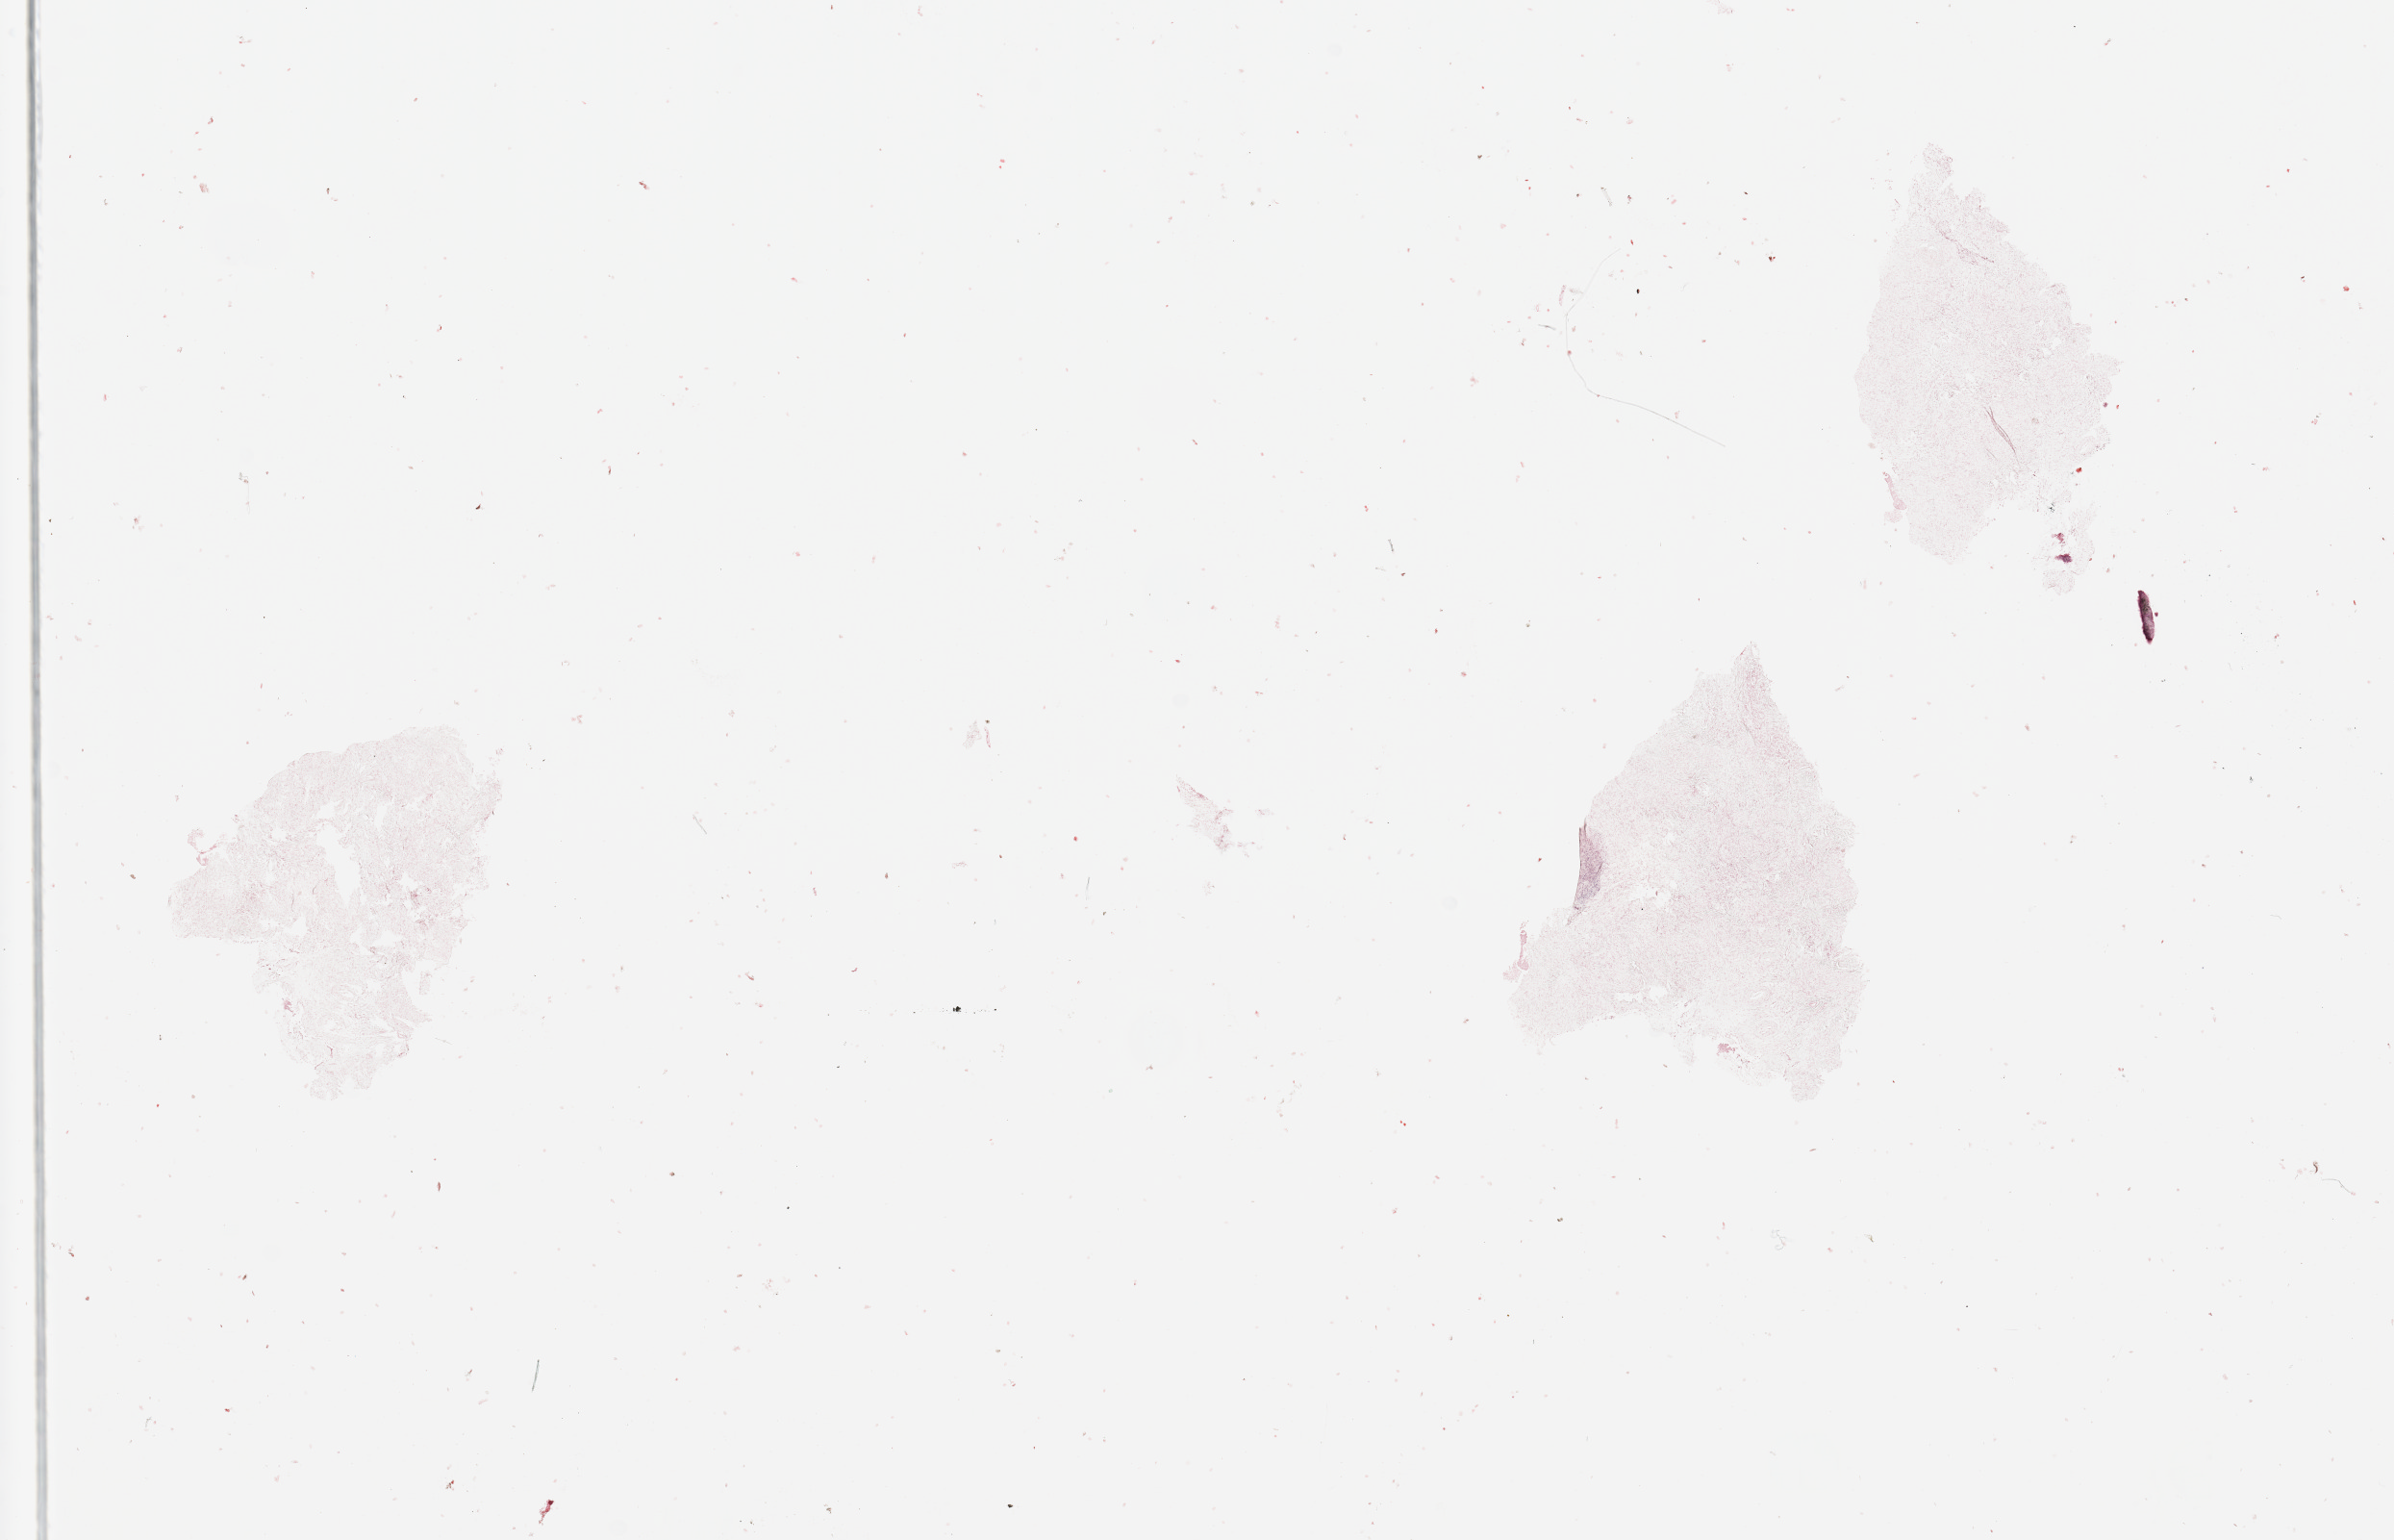
H&E-stained whole-slide image, shown as a low-resolution overview of the whole scanned area (about 19.7 x 12.7 mm); normal (non-tumour) tissue sample, uterus. Patient: female, age 83 years.
This section: normal (non-tumour) tissue from the same patient. Patient diagnosis: Endometrioid adenocarcinoma, NOS.